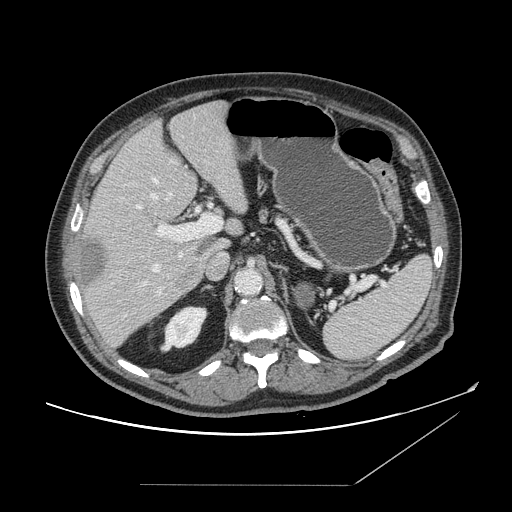
Contrast-enhanced abdominal CT, one axial slice. Slice 99 of 166 in the series (ordered by position). 120 kVp. Intravenous contrast given. Soft-tissue window (W 400 / L 40 HU). 2.5 mm slice thickness. 512 × 512 image matrix, field of view 416 × 416 mm. Male patient, age 80 years. From the clinical record (not read from this slice): diagnosis: colorectal cancer liver metastases, imaged before liver resection; multiple liver metastases: no.
Structures marked on this image (outlined manually by an expert reader):
- hepatic veins: bounding box <142,178,172,287> (left, top, right, bottom; pixels)
- liver: <79,102,249,347>
- planned liver remnant (the part of the liver to remain after resection): <91,101,247,256>
- portal vein (with intrahepatic branches): <138,206,222,295>
- liver metastasis: <83,237,108,287>